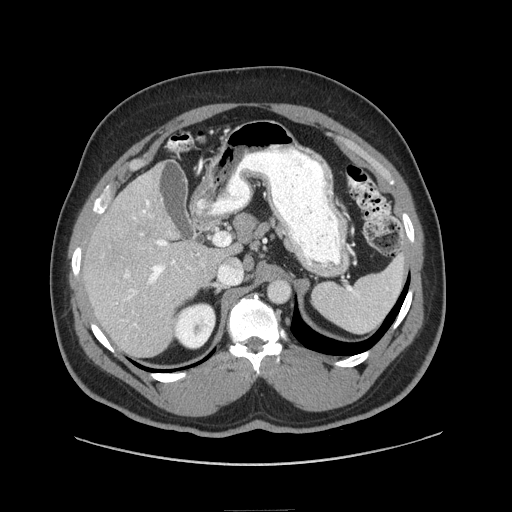
Contrast-enhanced abdominal CT (liver protocol), one axial slice; position 46 of 87 along the scan axis; soft-tissue window (W 400 / L 40 HU); 2.5 mm slice thickness; 512 × 512 image matrix. From the clinical record (not read from this slice): diagnosis: hepatocellular carcinoma (patient treated with transarterial chemoembolisation; whether this scan precedes or follows treatment is not stated here); TNM stage (as recorded): Stage-II; Child-Pugh class: A; tumour differentiation: moderately differentiated.
Annotated regions visible in this slice (semi-automatic segmentation, software-assisted and operator-edited):
- liver parenchyma outside the tumour (the mass and vessels are separate outlines, so this box may not span the whole liver): bounding box <82,163,228,356> (left, top, right, bottom; pixels)
- liver vessels: <124,199,204,327>